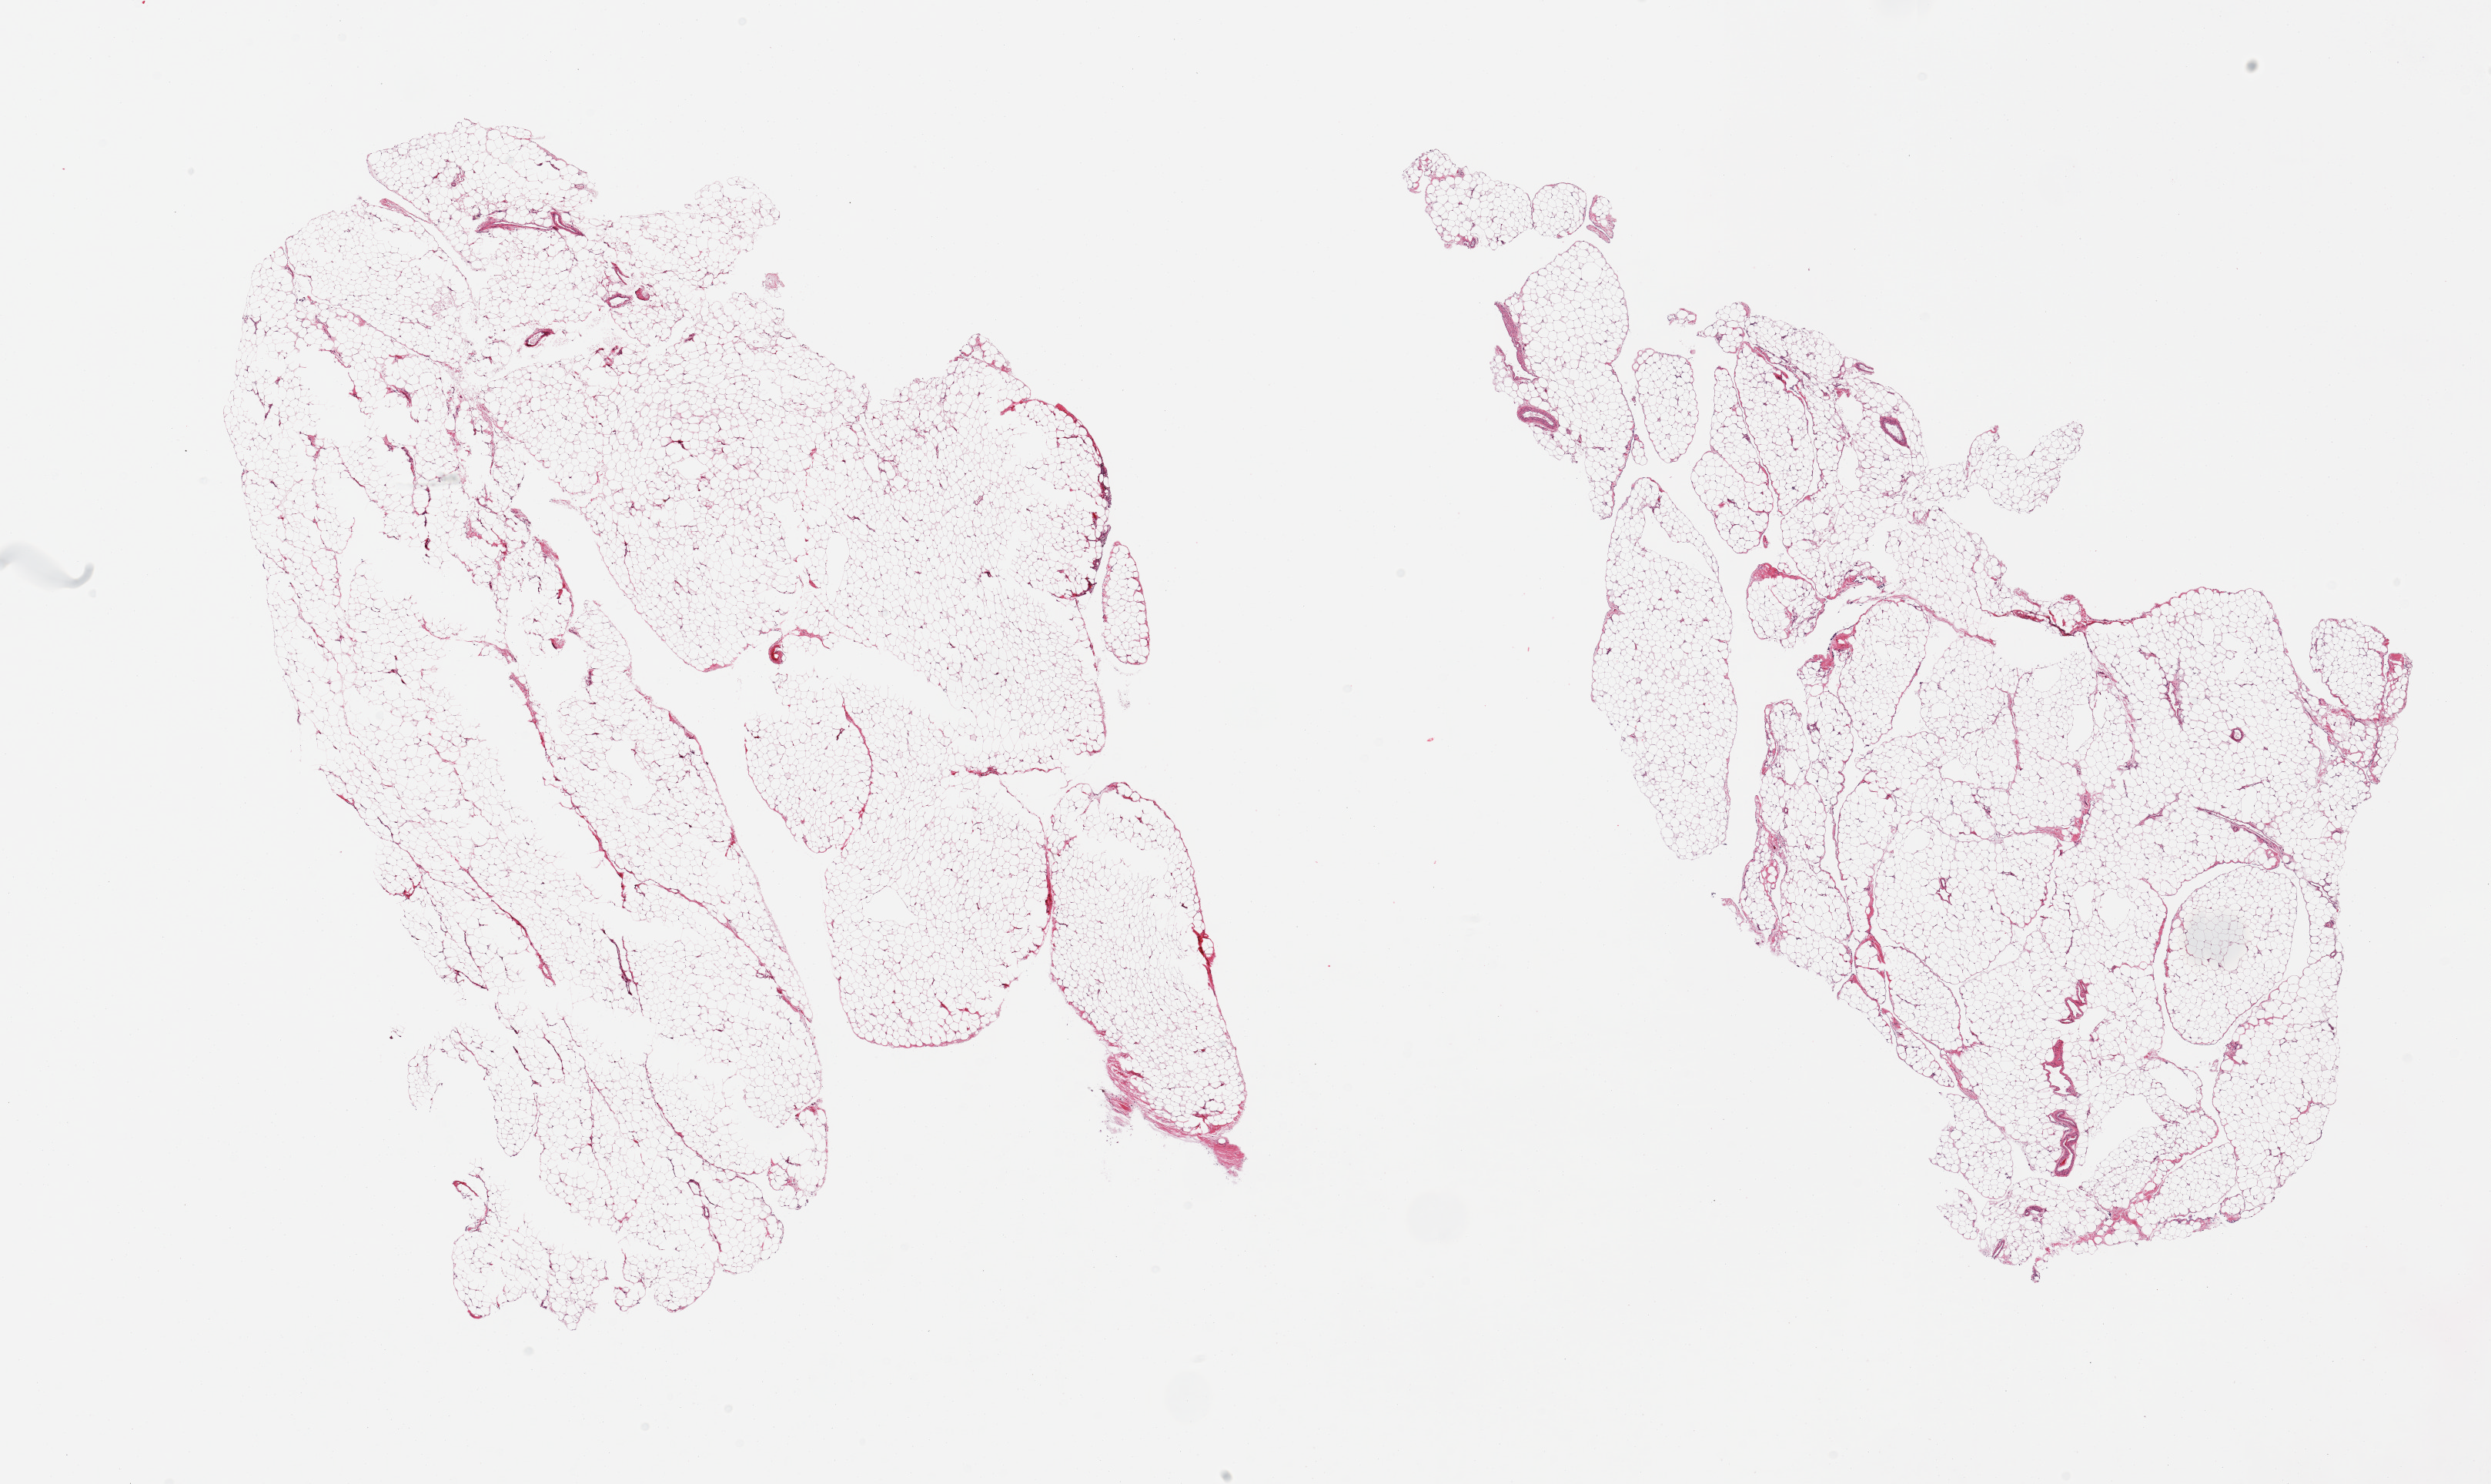
Haematoxylin and eosin whole-slide image, a low-resolution overview of the entire scanned area, about 25.6 x 15.2 mm; PAXgene-fixed paraffin-embedded (PFPE) section; section of omentum (target tissue); donor tissue sample. Donor sex: female.
- reviewer comment on this tissue sample: 2 pieces